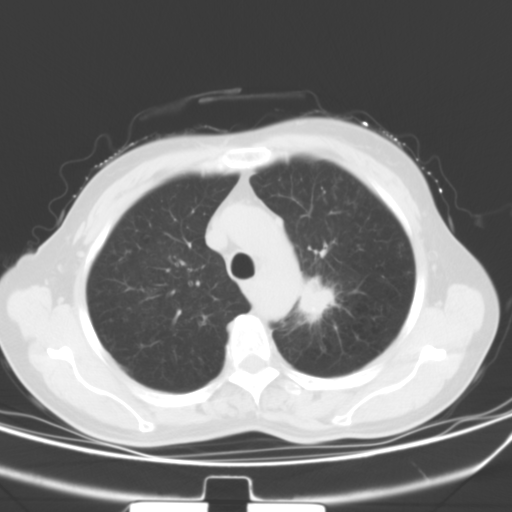
Chest CT, one axial slice; position 43 of 53 along the scan axis; 120 kVp; lung window (W 1500 / L -600 HU); 5 mm slice thickness; 512 × 512 image matrix. Female patient, age 60 years. Case-level facts recorded for this patient, not image findings: clinical TNM (as recorded): T1b N0 M0.
Structures marked on this image (bounding box drawn by a radiologist):
- lung tumour (recorded histology: squamous cell carcinoma): box from (x=287, y=275) to (x=342, y=322) px